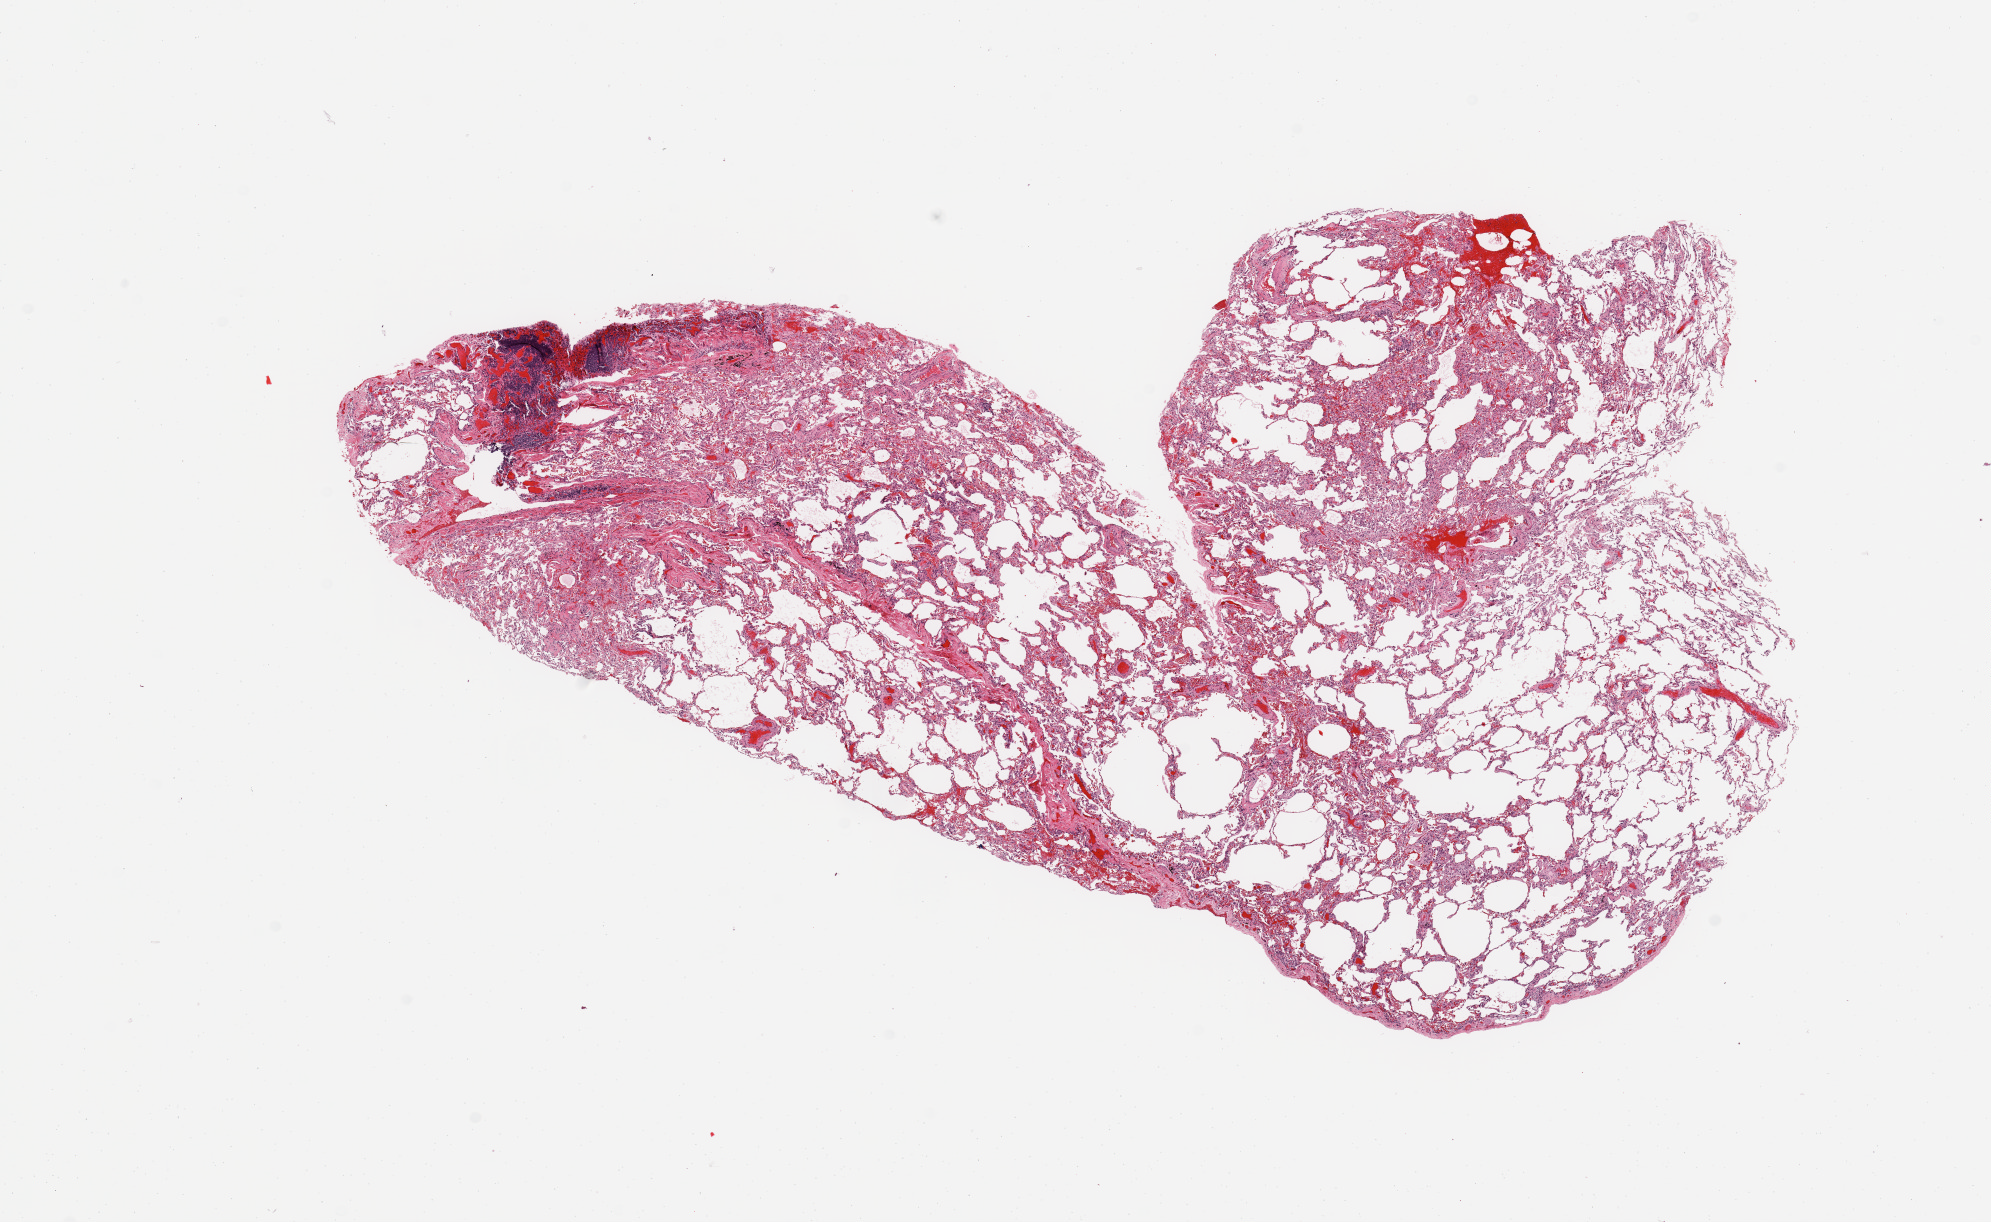
Whole-slide histology image, H&E — low-resolution overview of the scanned area, about 15.8 x 9.7 mm (slide scanned at 20x); normal (non-tumour) tissue sample, sampled site: lung. Female, 61 y/o.
This section: normal (non-tumour) tissue from the same patient. Patient diagnosis: Adenocarcinoma, NOS.